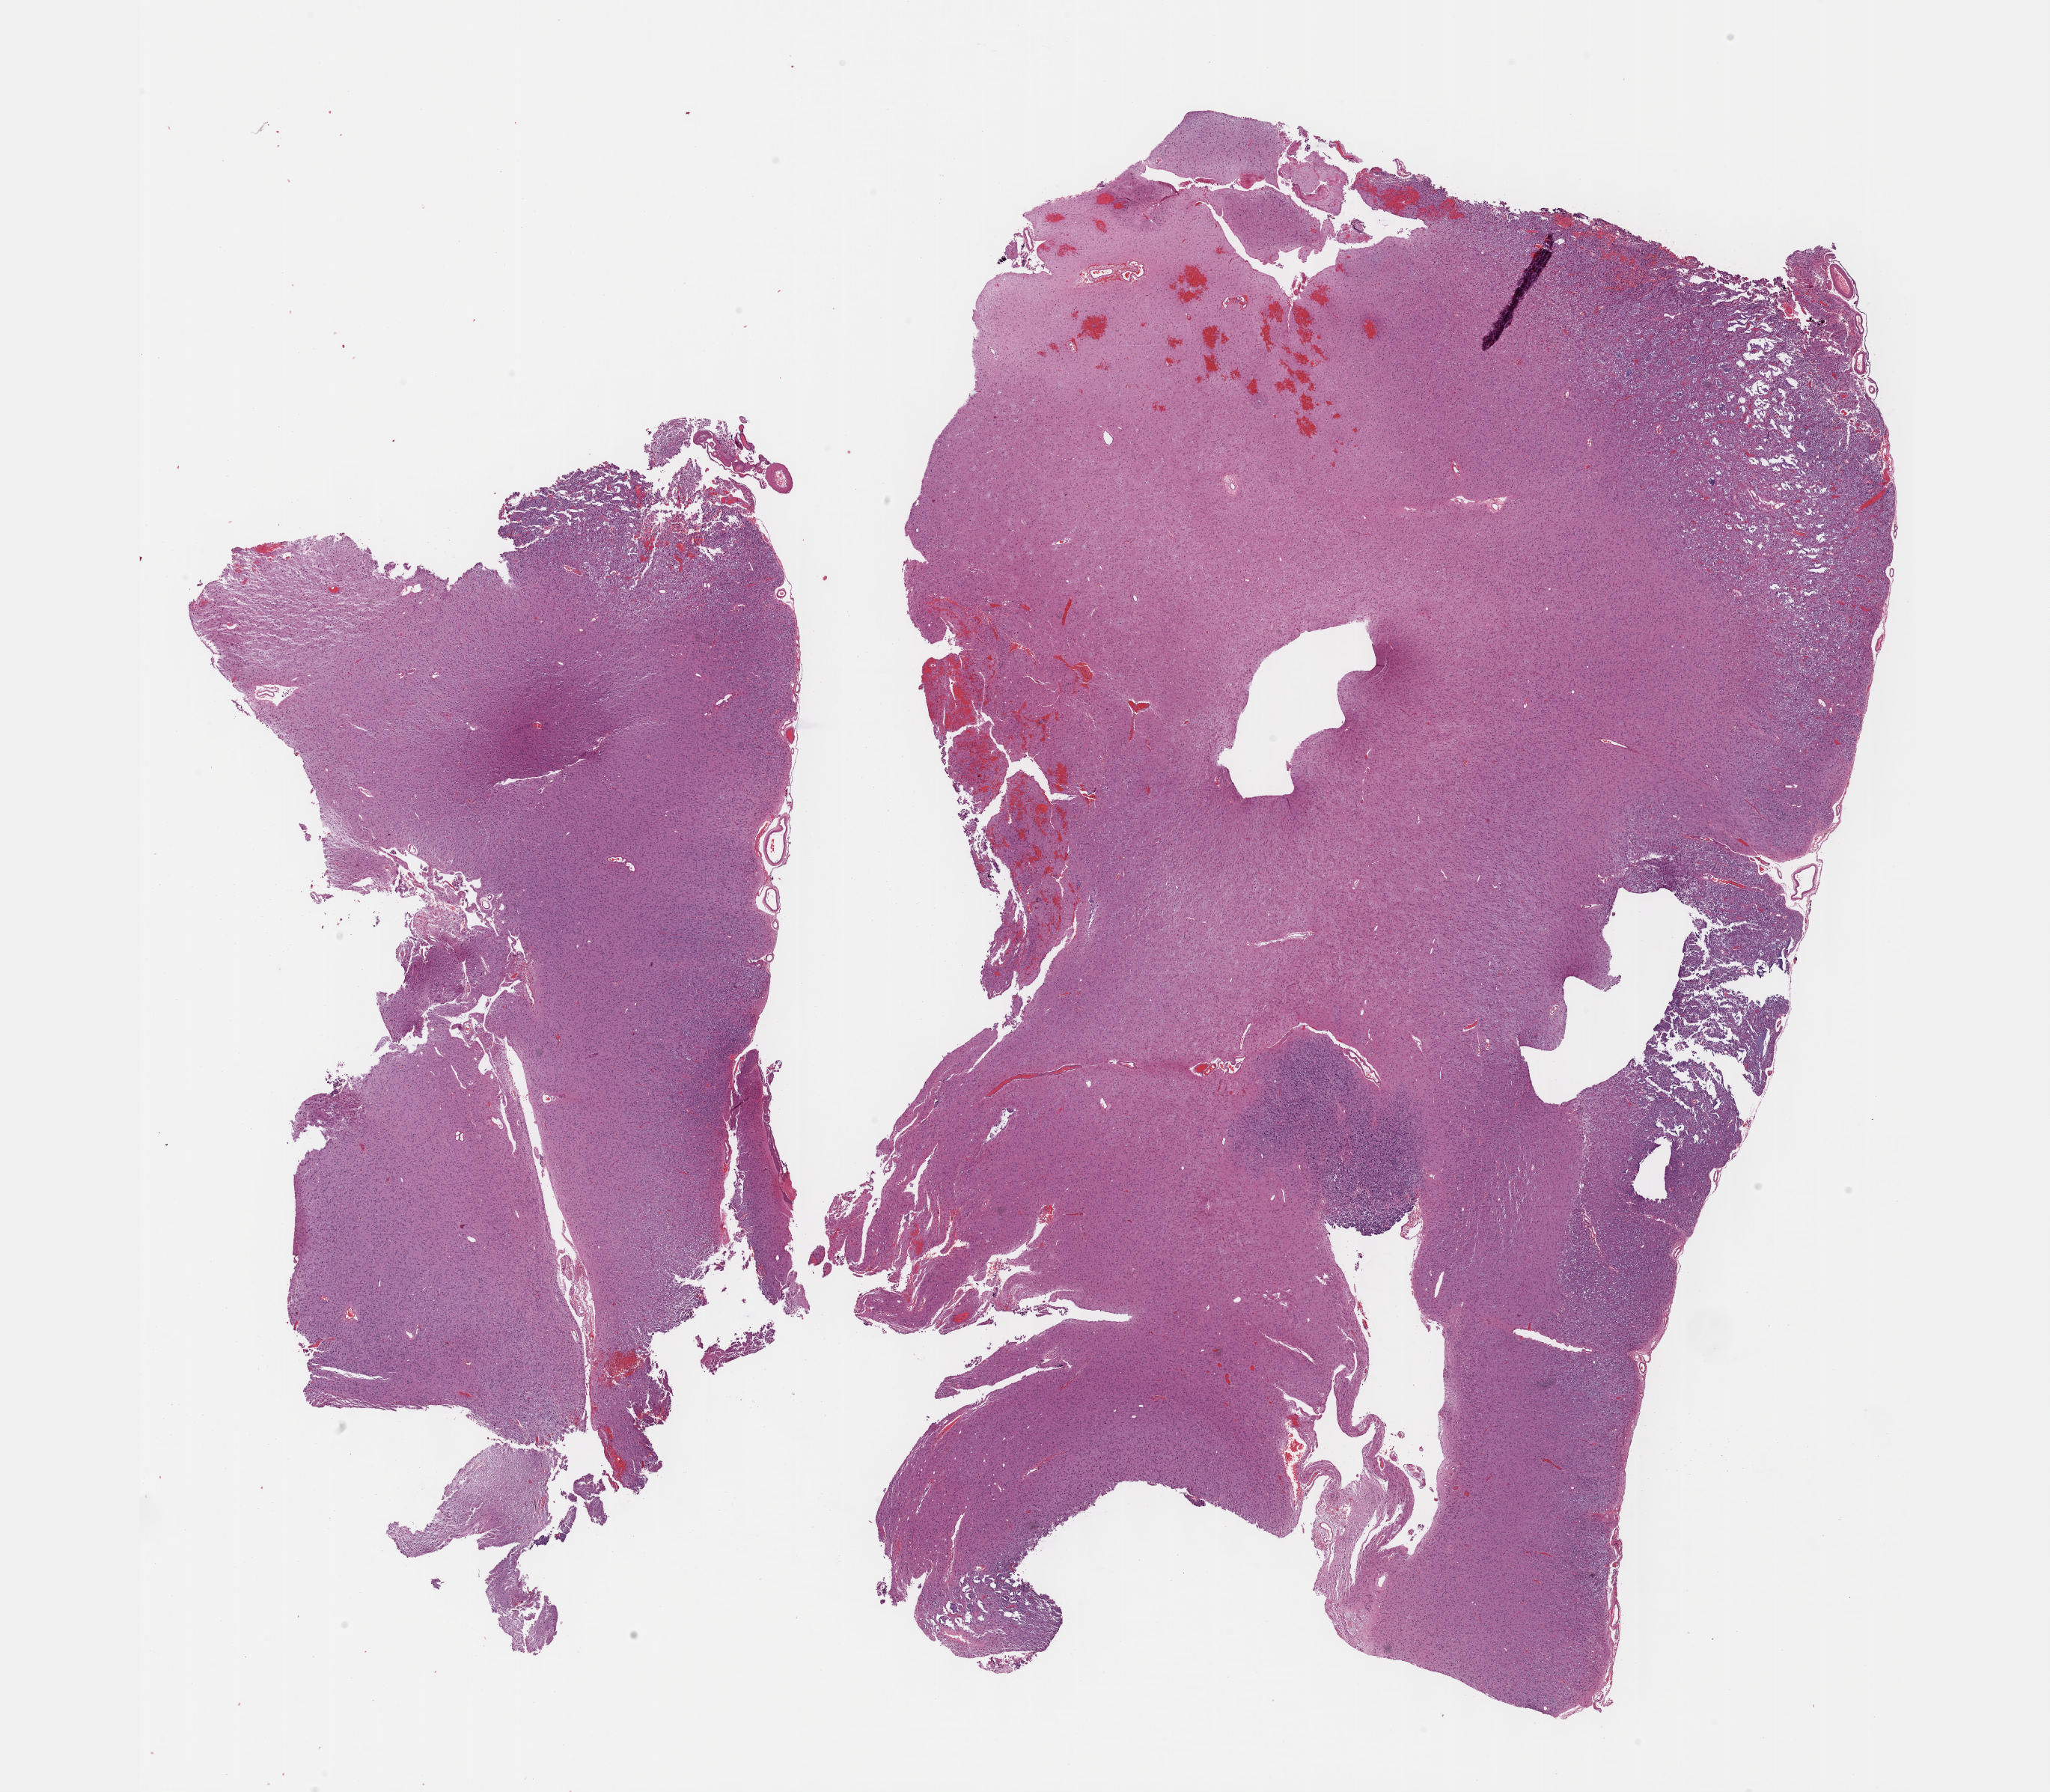
Whole-slide histology image, H&E-stained, low-resolution overview of the scanned area, about 22.1 x 19.3 mm. Formalin-fixed paraffin-embedded (FFPE) diagnostic section. Sample: primary tumour, brain. Male, age 59 years at initial diagnosis. Histologic grade: G3 (poorly differentiated).
• histologic diagnosis: Oligodendroglioma, anaplastic (cerebrum)